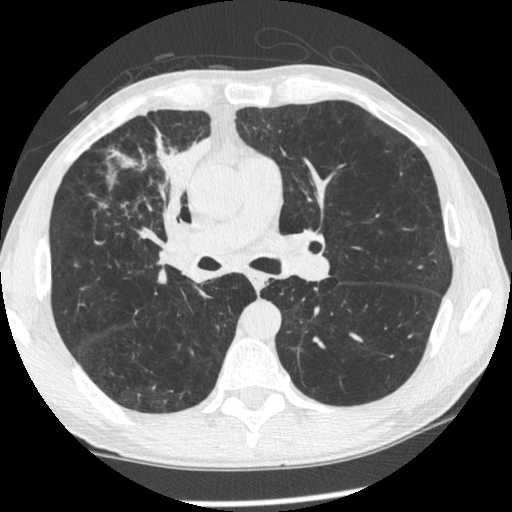
Low-dose screening chest CT, one axial slice; slice 136 of 261 in the series (ordered by position); 120 kVp; lung window (W 1500 / L -600 HU); 512 × 512 image matrix.
Outlined on this slice (manually delineated by an expert):
- lesion 1 (tumor, upper lobe of right lung): bounding box [x1, y1, x2, y2] px = [155, 131, 212, 236]